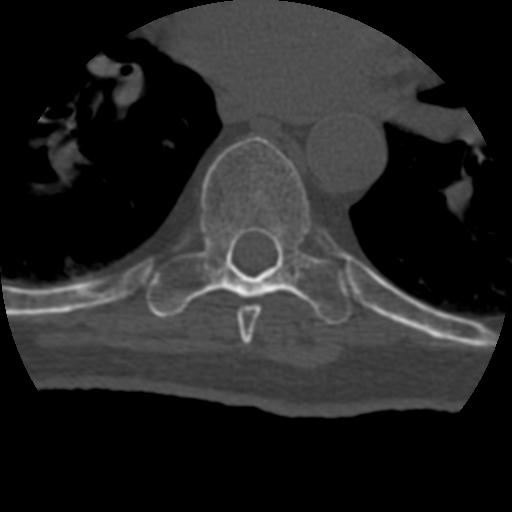
CT including the spine, one axial slice. Slice 265 of 399 in the series (ordered by position). Reconstruction kernel STANDARD. Bone window (W 1800 / L 400 HU). 1.25 mm slice thickness. 512 × 512 image matrix, field of view 160 × 160 mm. Patient age 69 years. From the clinical record (not read from this slice): primary cancer: prostate.
Outlined on this slice (semi-automatic segmentation, software-assisted and operator-edited):
- T7 vertebra: bounding box [x1, y1, x2, y2] px = [237, 305, 261, 344]
- T8 vertebra: [147, 136, 353, 324]